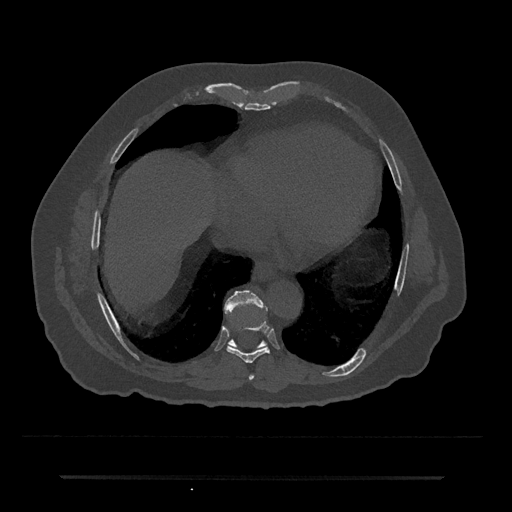
CT including the spine, one axial slice; position 316 of 797 along the scan axis; reconstruction kernel Br40s/3; bone window (W 1800 / L 400 HU); 0.5 mm slice thickness; 512 × 512 image matrix, field of view 437 × 437 mm. Male patient, age 69 years. Case-level facts recorded for this patient, not image findings: primary cancer: prostate.
Annotated regions visible in this slice (semi-automatically segmented with operator editing):
- T7 vertebra: bounding box <249,374,255,380> (left, top, right, bottom; pixels)
- T8 vertebra: <227,321,270,363>
- T9 vertebra: <224,290,266,345>